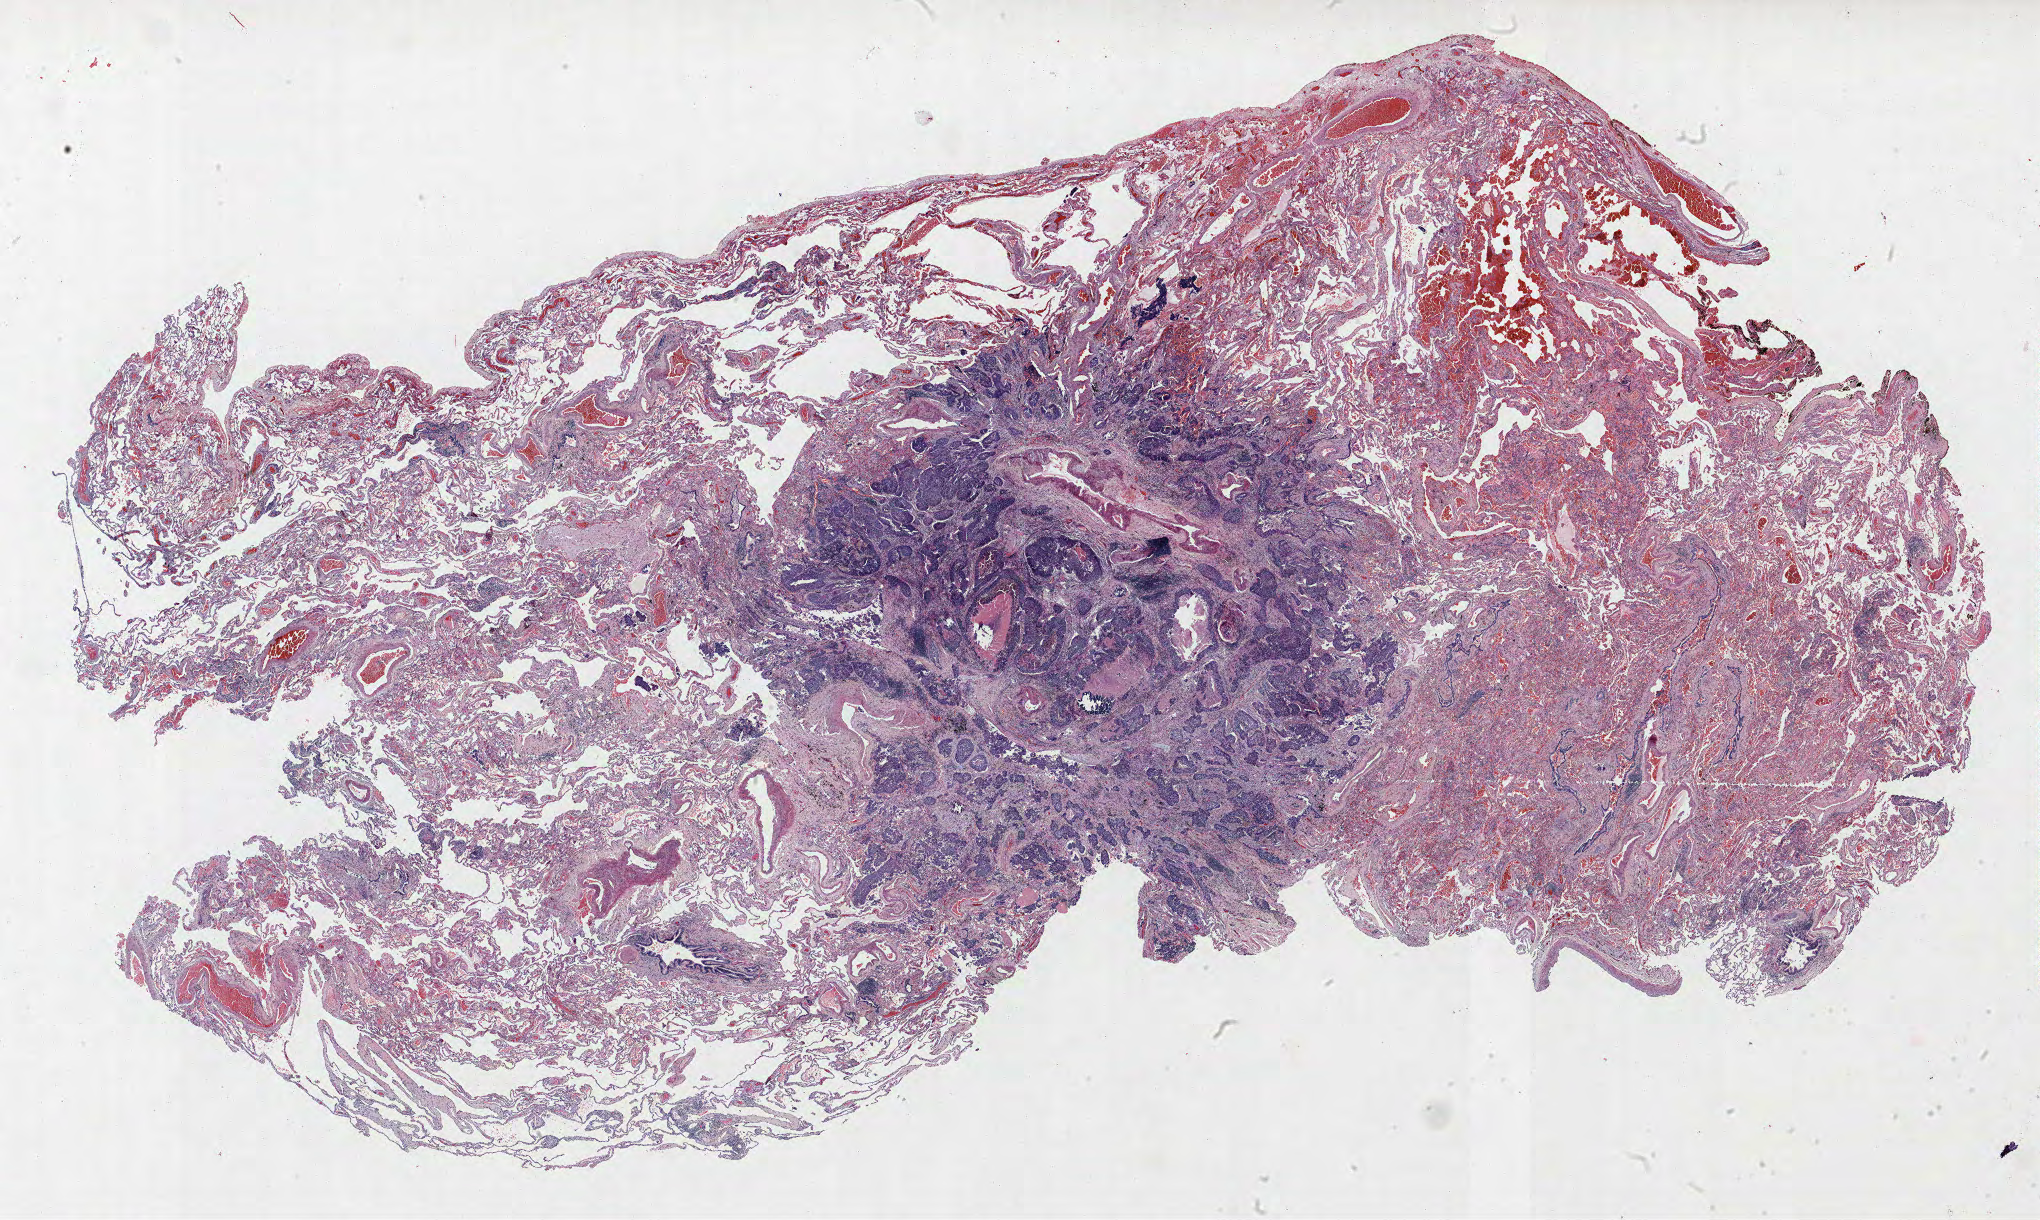
H&E whole-slide image — whole scanned area (about 32.6 x 19.5 mm, acquisition: 40x scan) shown as a low-resolution overview; formalin-fixed paraffin-embedded (FFPE) section; lung tissue. Female patient, aged 59 at enrolment. Current smoker at enrolment.
Participant's lung-cancer diagnosis: Adenocarcinoma, NOS. Note: participant had 2 primary lung cancers recorded; fields above describe the first.